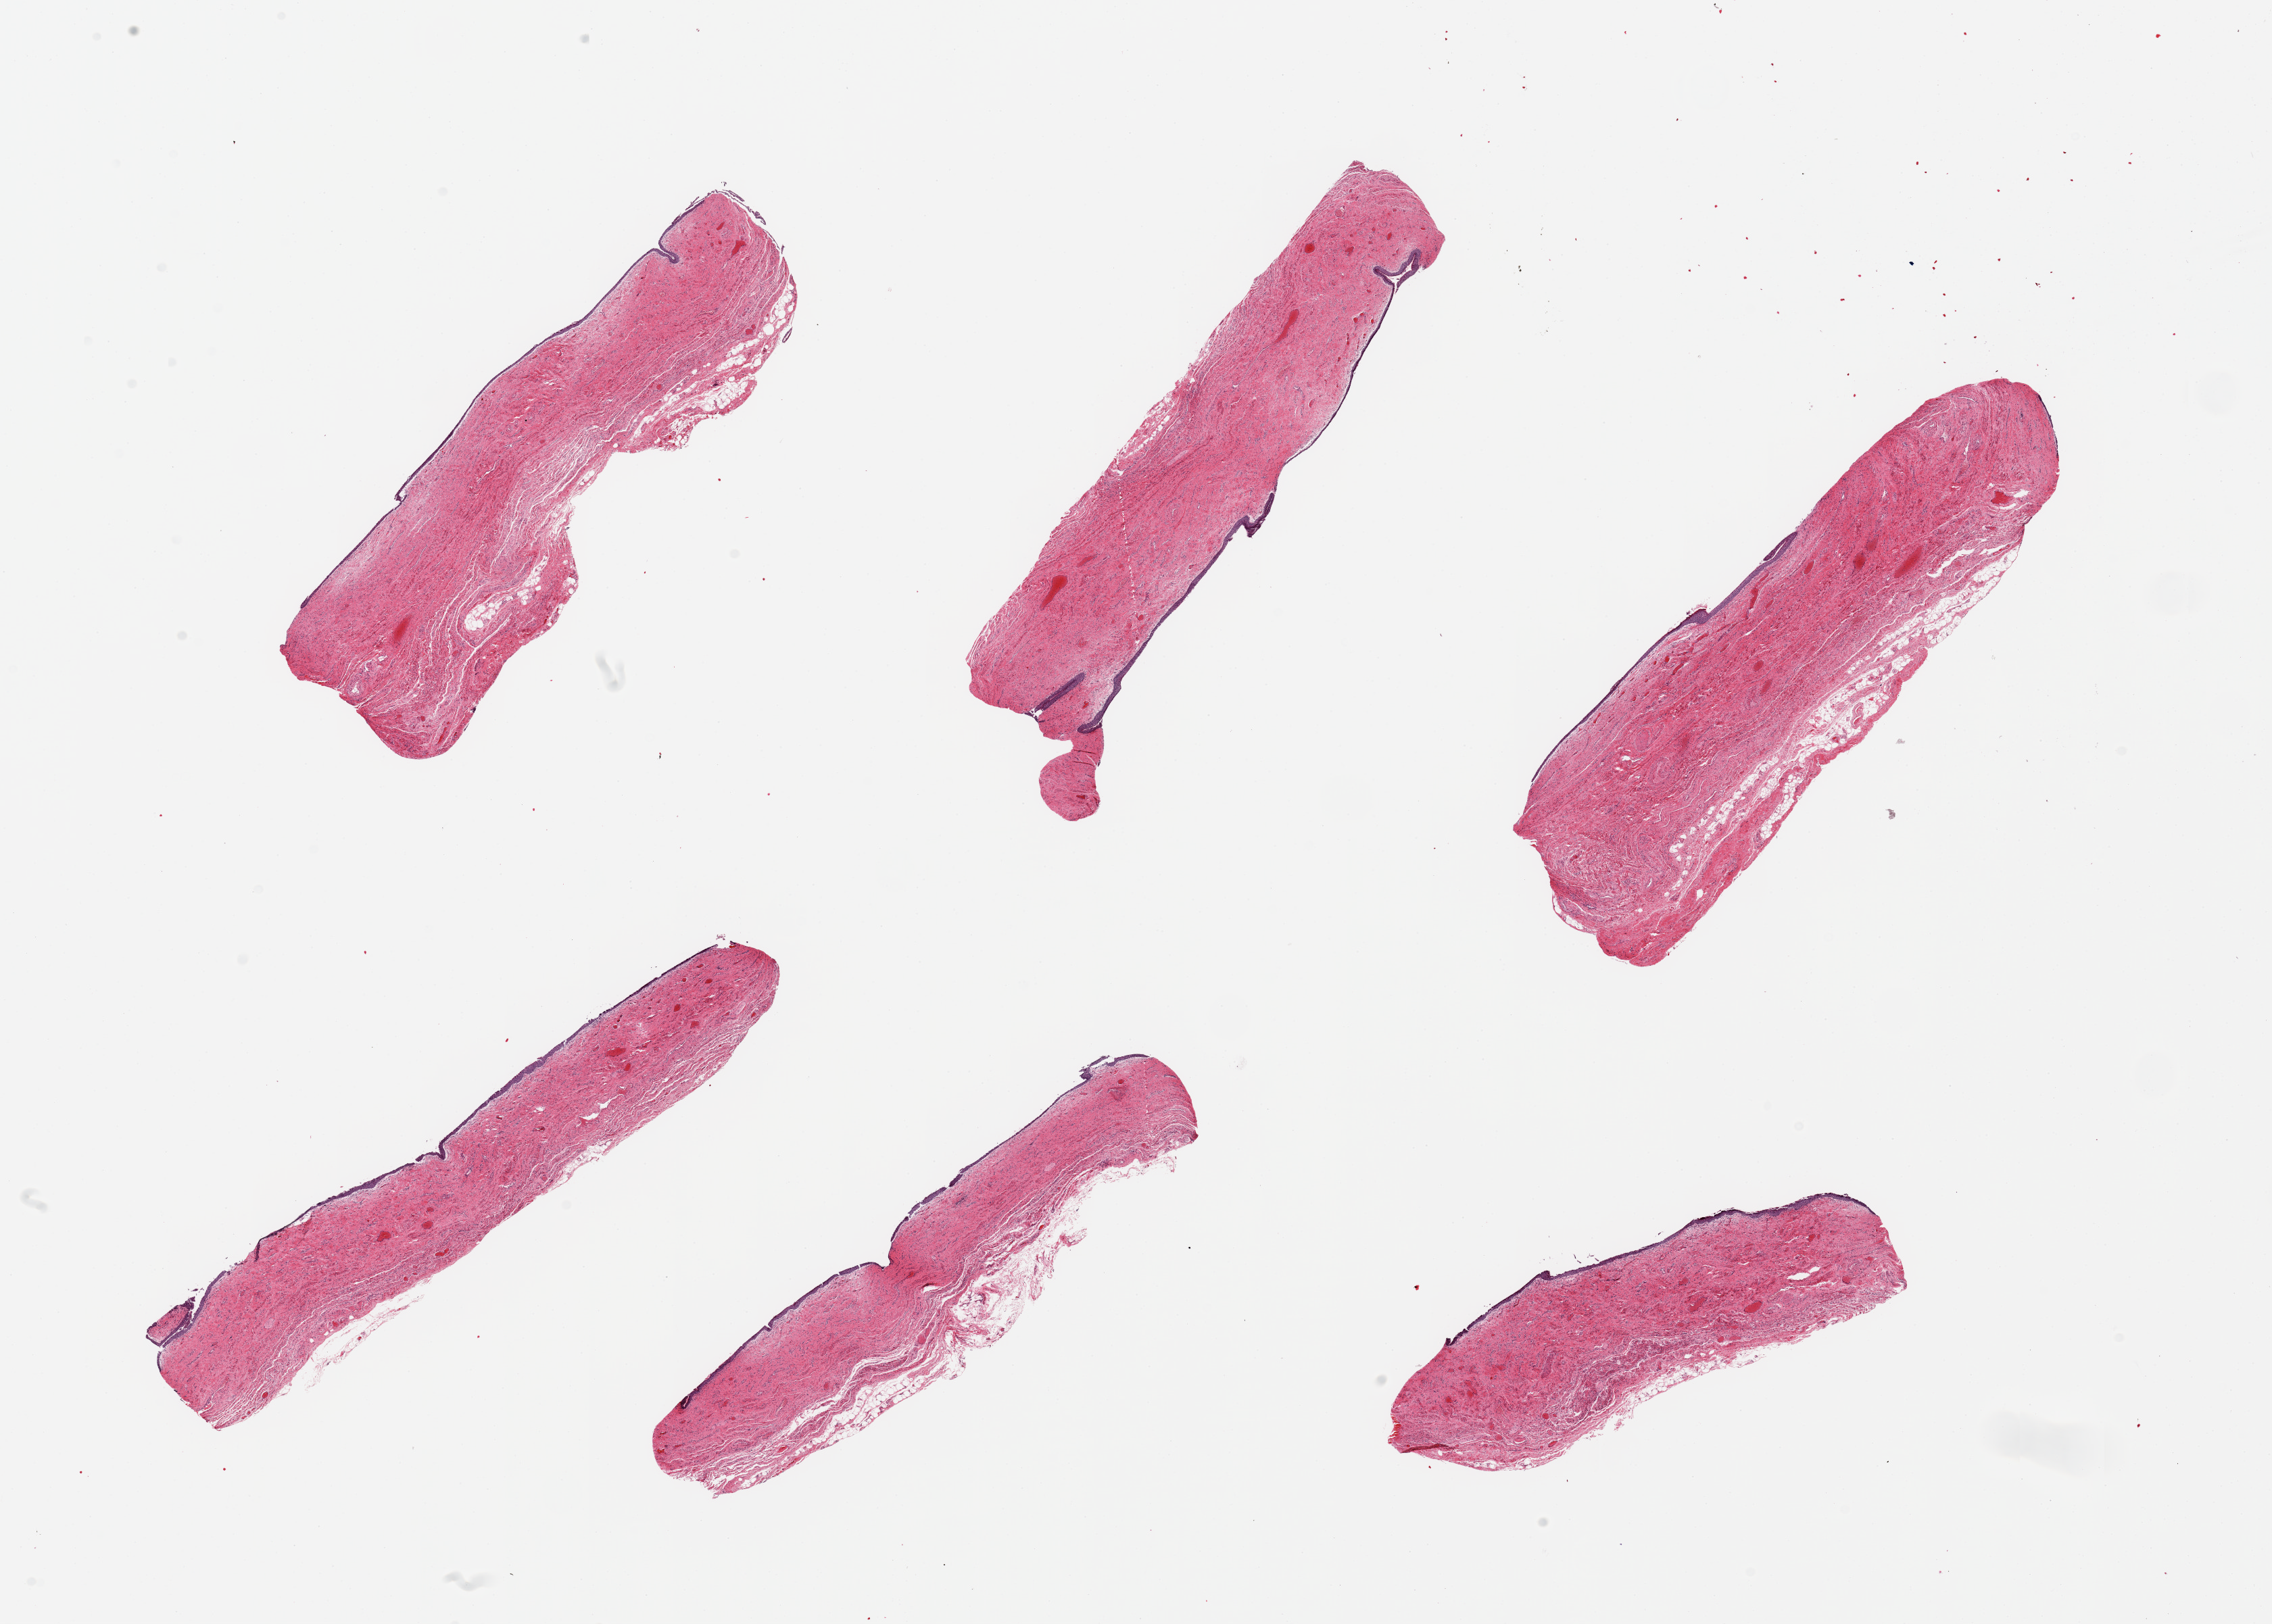
Whole-slide image, H&E stain — whole scanned area (about 26.6 x 19.0 mm) shown as a low-resolution overview, PAXgene-fixed paraffin-embedded (PFPE) section, section of vagina (target tissue), tissue donor sample. Donor sex: female.
* reviewer comment on this tissue sample: 6 pieces; some sloughing and atrophy of squamous epithelium